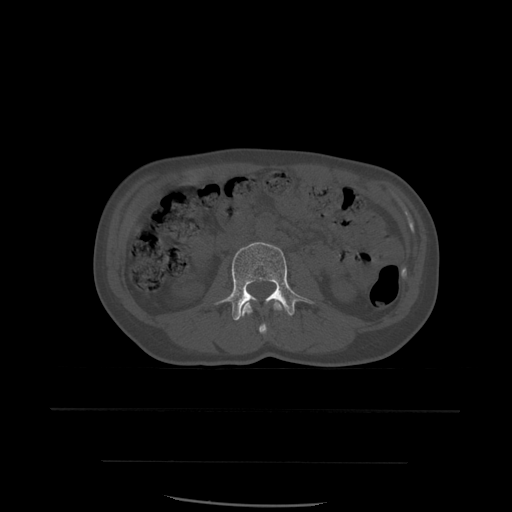
CT including the spine, one axial slice. Slice 204 of 574 in the series (ordered by position). Bone window (W 1800 / L 400 HU). 1.25 mm slice thickness. 512 × 512 image matrix, field of view 392 × 392 mm. Patient age 48 years. Case-level facts recorded for this patient, not image findings: primary cancer: lung.
Structures marked on this image (semi-automatically segmented with operator editing):
- L2 vertebra: bounding box [x1, y1, x2, y2] px = [240, 301, 283, 335]
- L3 vertebra: [216, 242, 313, 321]